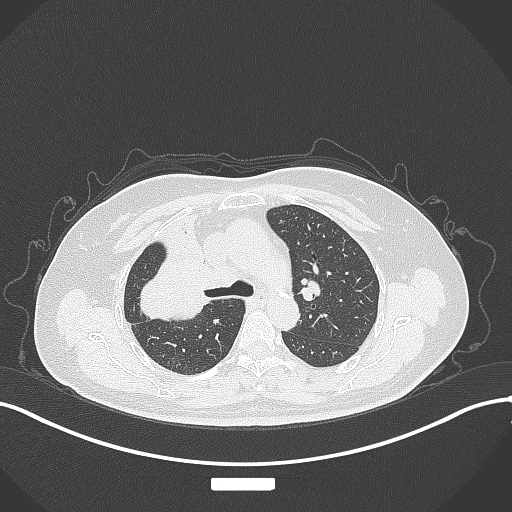
Chest CT, one axial slice; slice 214 of 309 in the series (ordered by position); reconstruction kernel B70f; 120 kVp; lung window (W 1500 / L -600 HU); 1 mm slice thickness; 512 × 512 image matrix, field of view 400 × 400 mm. Female patient, age 60 years. Case-level facts recorded for this patient, not image findings: clinical TNM (as recorded): T3 N1 M1.
Structures marked on this image (bounding box drawn by a radiologist):
- lung tumour (recorded histology: adenocarcinoma): box from (x=125, y=242) to (x=217, y=328) px